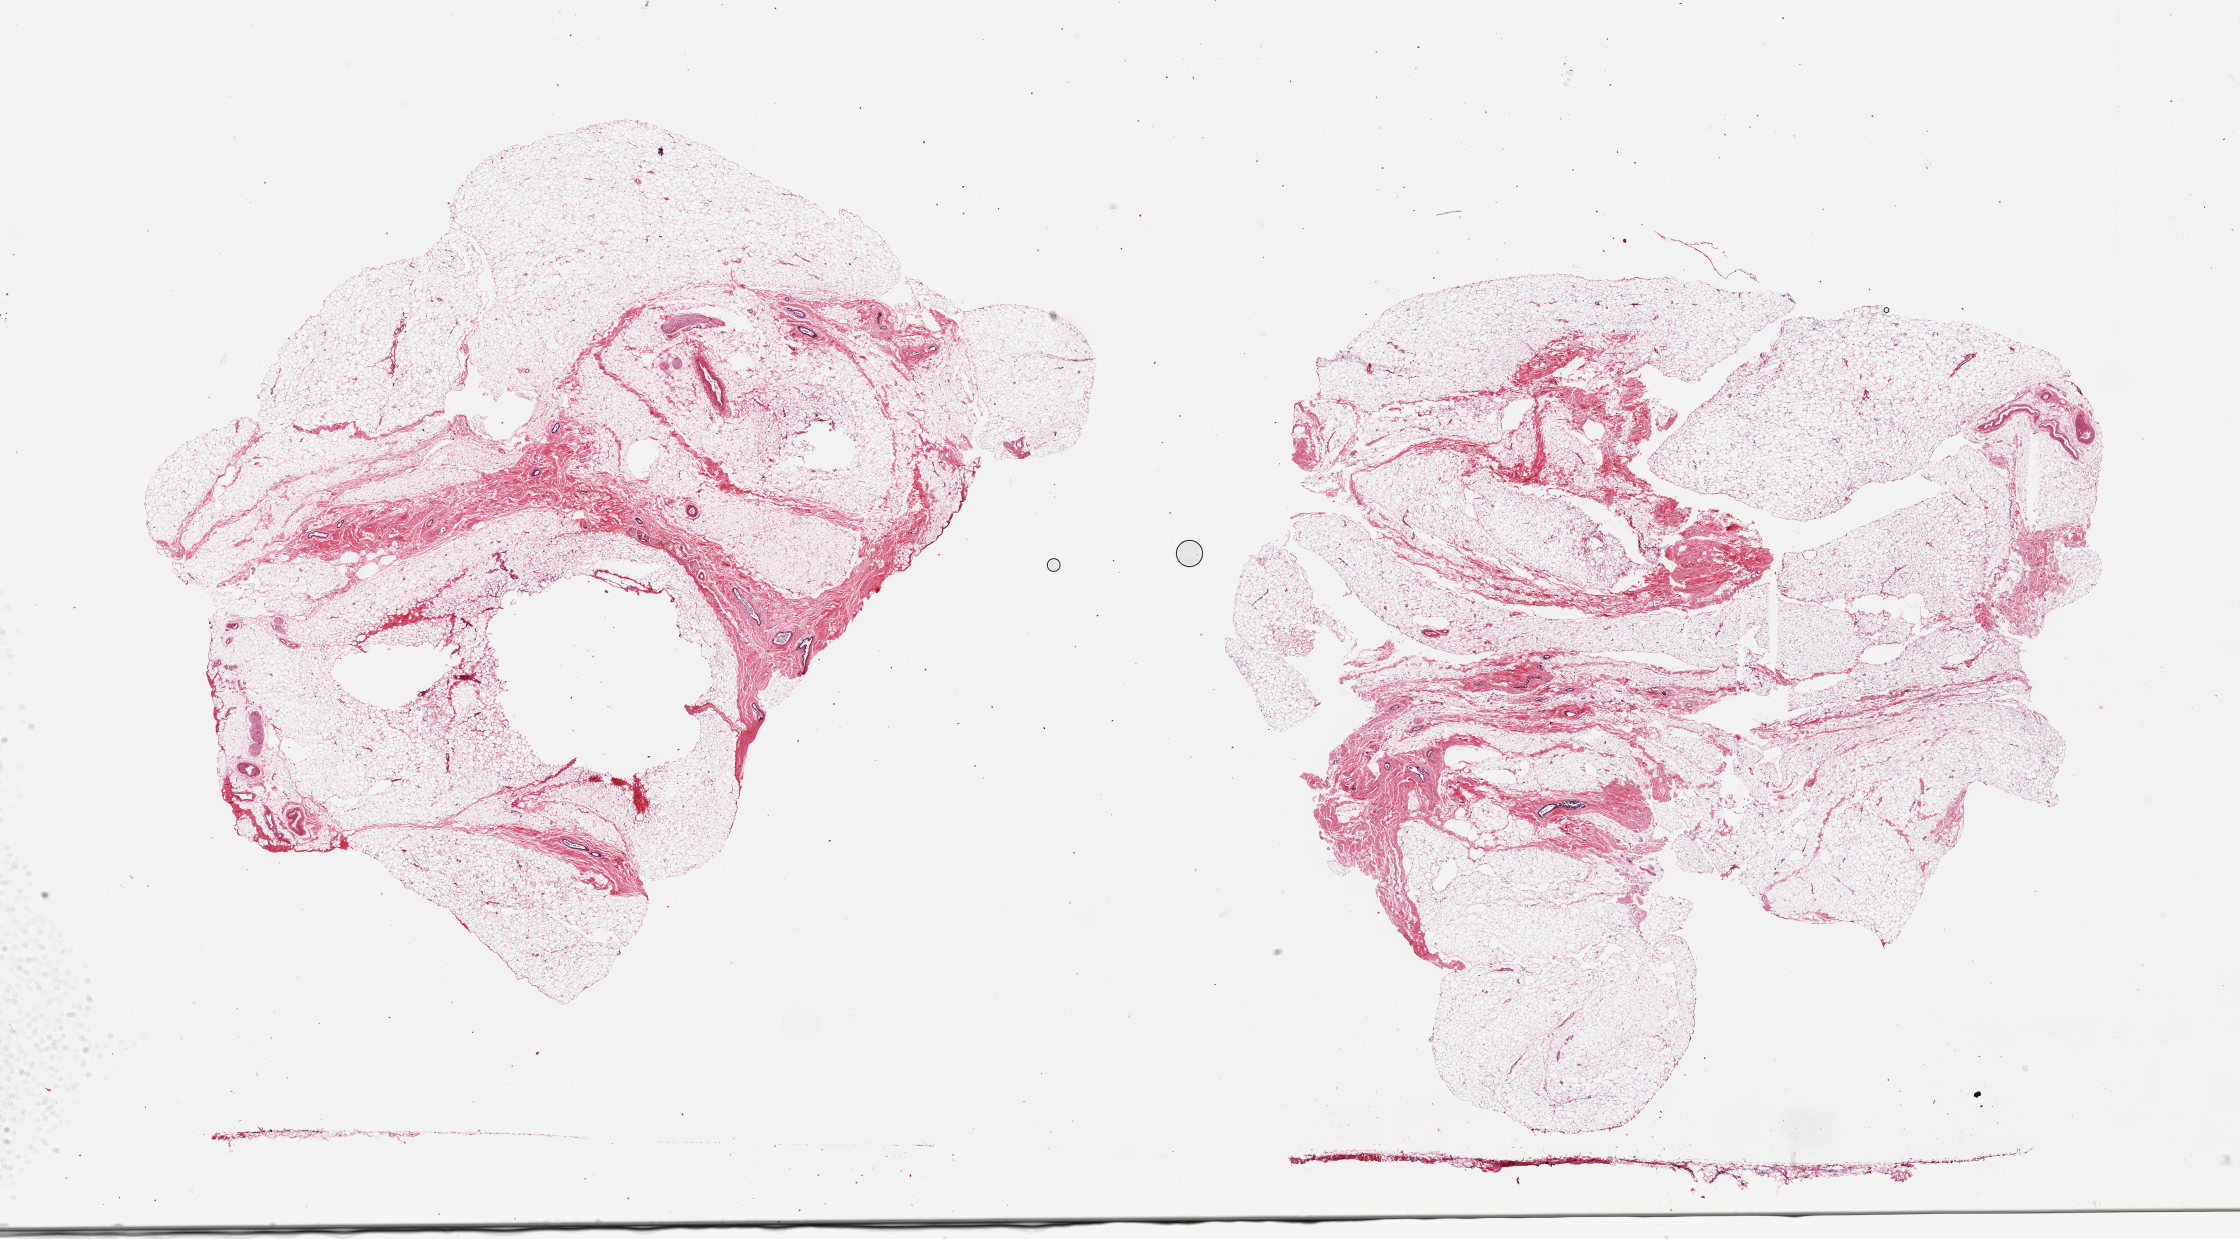
H&E whole-slide image, shown as a low-resolution overview of the whole scanned area (about 35.4 x 19.6 mm, from a 20x scan). PAXgene-fixed paraffin-embedded (PFPE) section. Section of breast (target tissue). Donor tissue sample. Male donor.
- reviewer comment on this tissue sample: 2 pieces; 70-80% fat, remainder is fibrocollagenous tissue with scattered small ducts/vessels/nerve